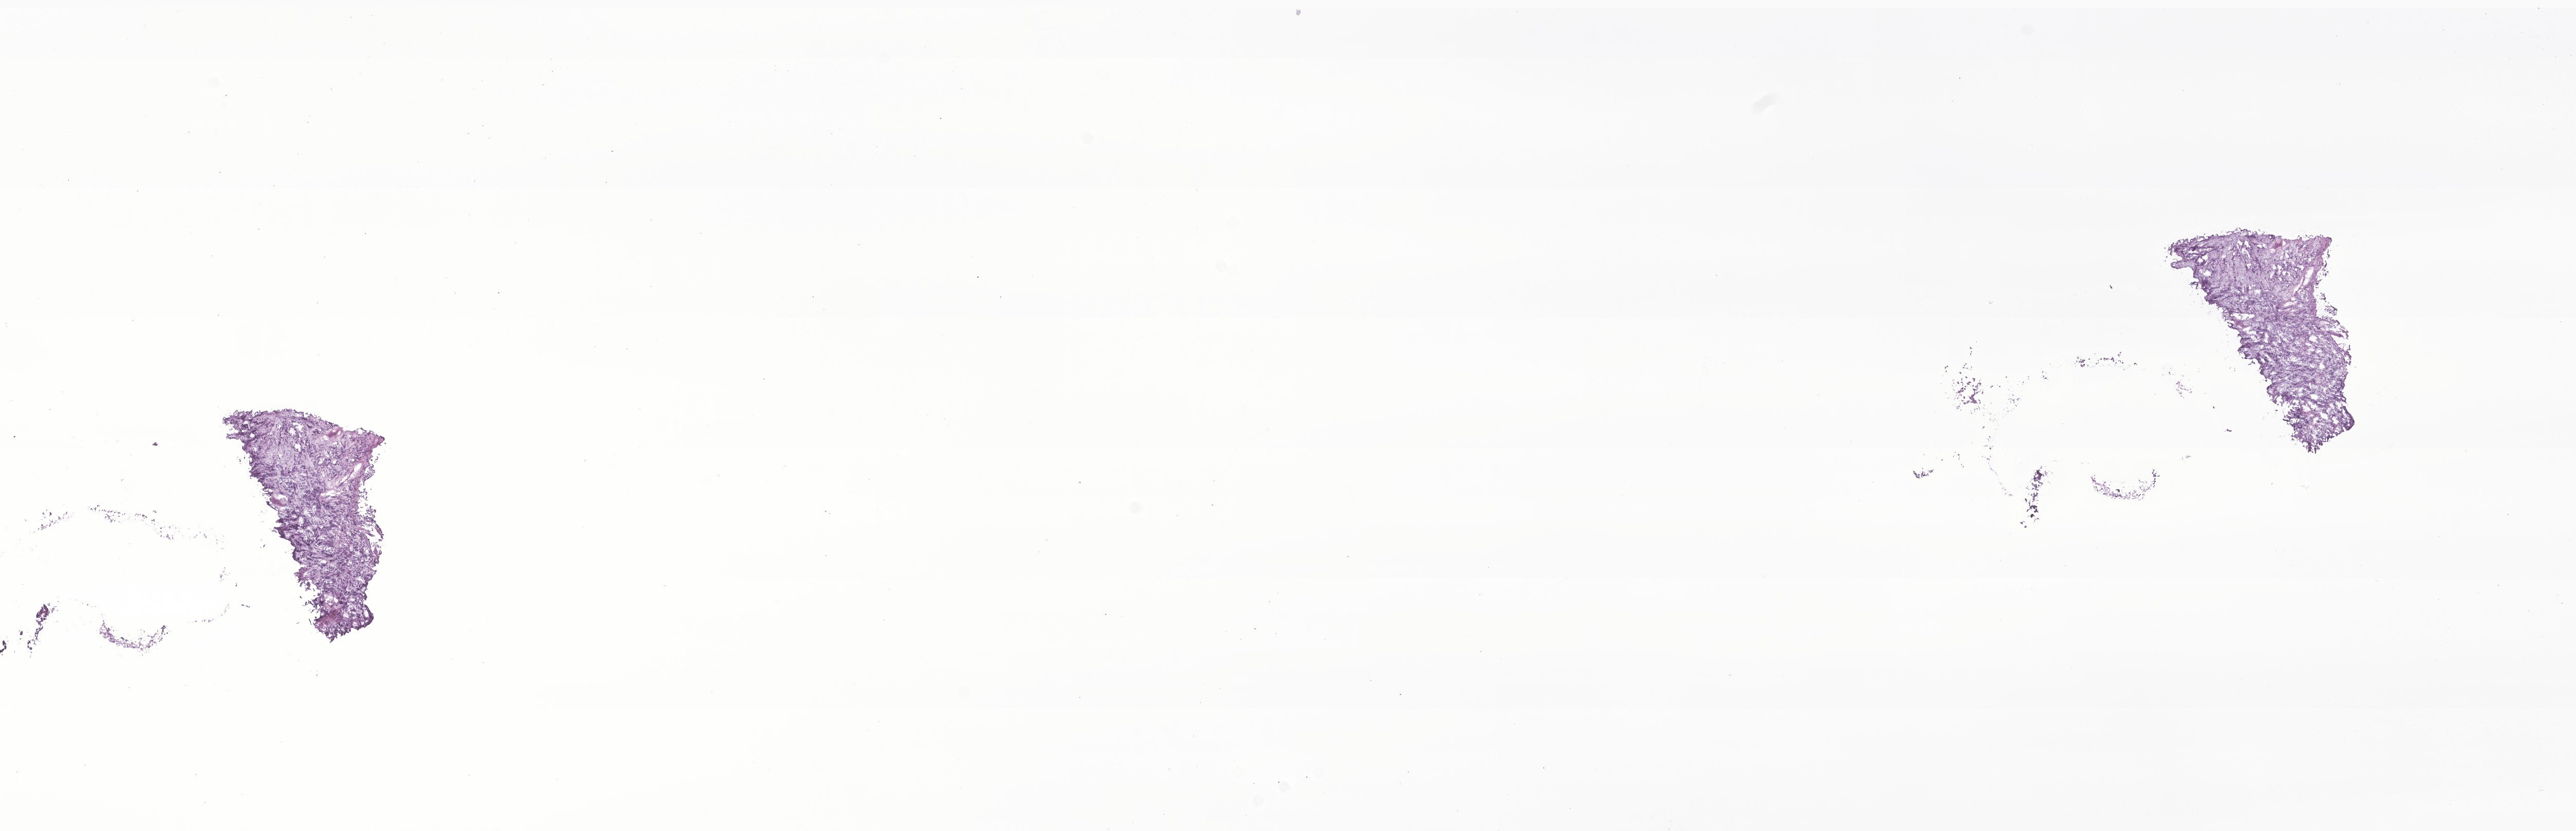
Haematoxylin and eosin whole-slide image of tumor tissue from the cerebellum — low-resolution overview of the scanned area, about 21.1 x 6.8 mm. Frozen section (OCT-embedded). Patient: female, age 58 months (4 years 10 months).
Diagnosis (ICD-O-3 morphology term): Medulloblastoma, NOS.